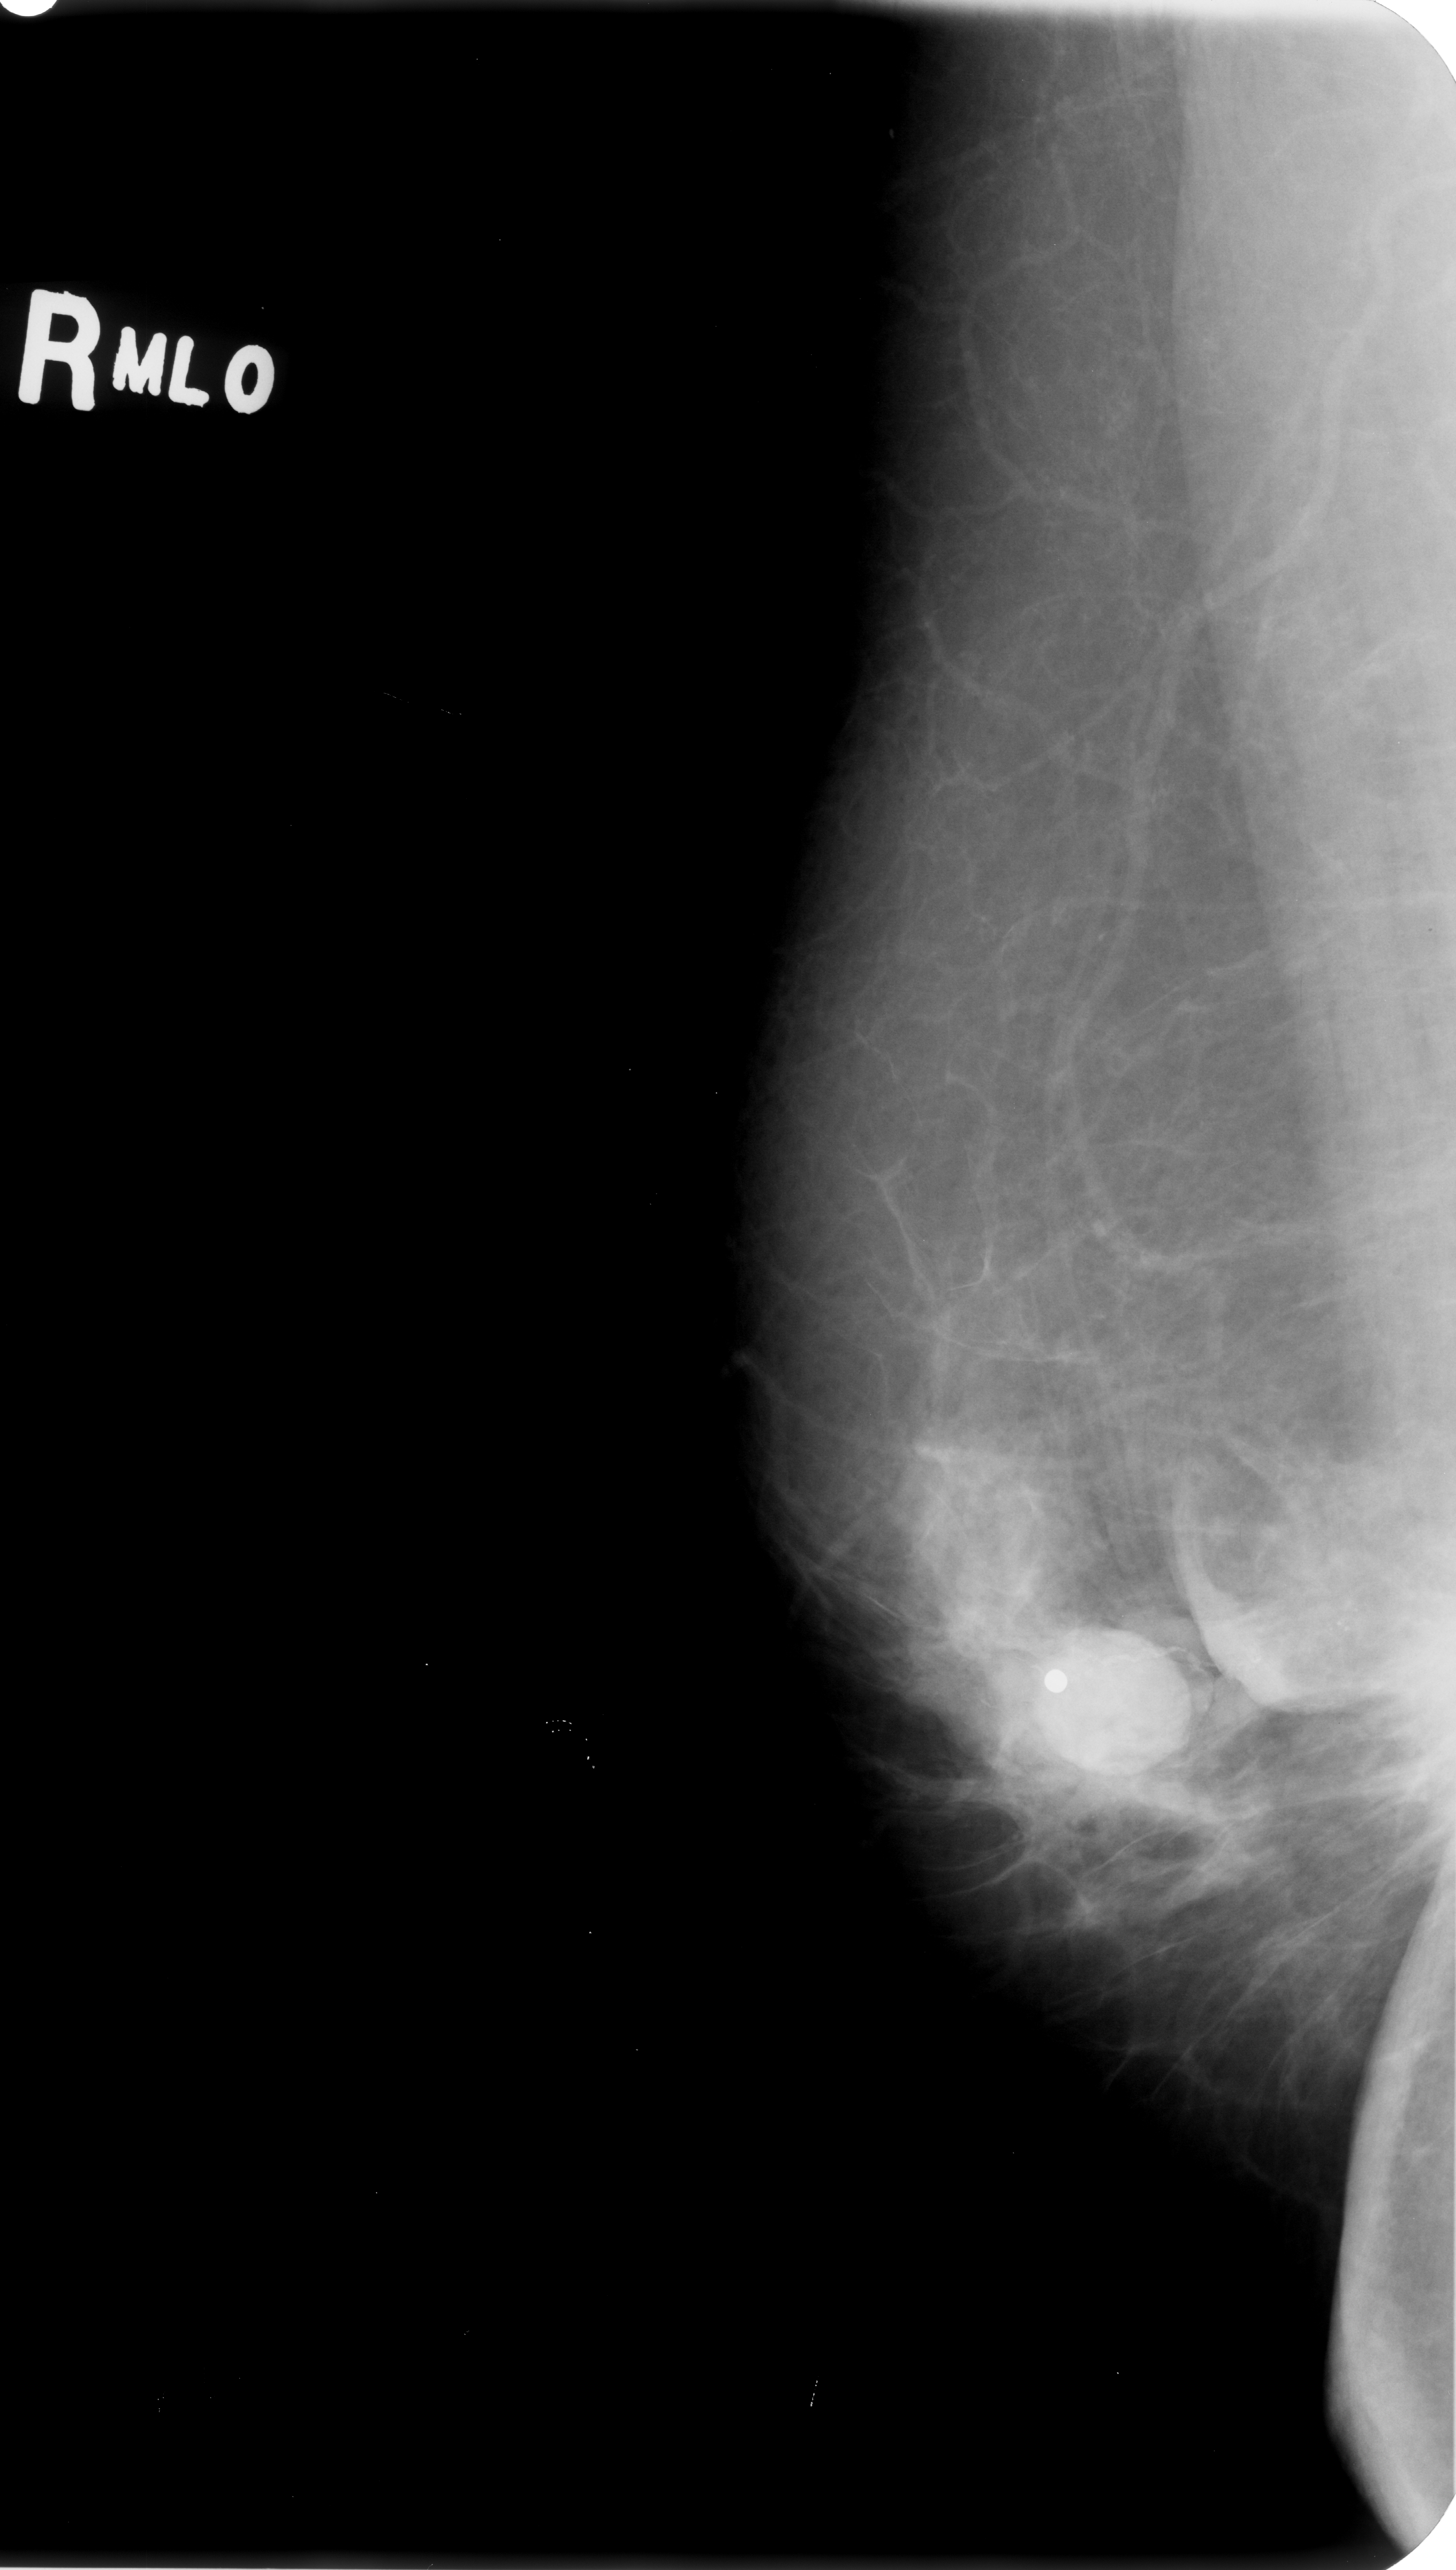
Mammogram (digitized film). Right breast. Mediolateral oblique (MLO) view. BI-RADS breast density category 2 (scale 1–4). 1456 × 2570 image matrix.
Expert-marked regions of interest on this film, with their recorded descriptors:
- calcifications, morphology pleomorphic / fine linear branching, distribution clustered / linear; BI-RADS assessment category 5; pathology result (as recorded, not read from the image): malignant: bounding box [x1, y1, x2, y2] px = [972, 1422, 1453, 1886]